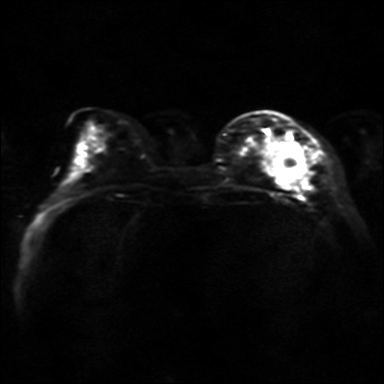
Breast MRI, one axial slice. Slice 12 of 36 in the series (ordered by position). Diffusion-weighted series; image 2 of 4 stored at this slice position (different b-values; order by instance number). 3 T. 384 × 384 image matrix, field of view 320 × 320 mm. Female patient.
Annotated regions visible in this slice (expert manual segmentation):
- tumour on diffusion-weighted imaging: bounding box (x1, y1, x2, y2) in pixels: (270, 141, 304, 185)